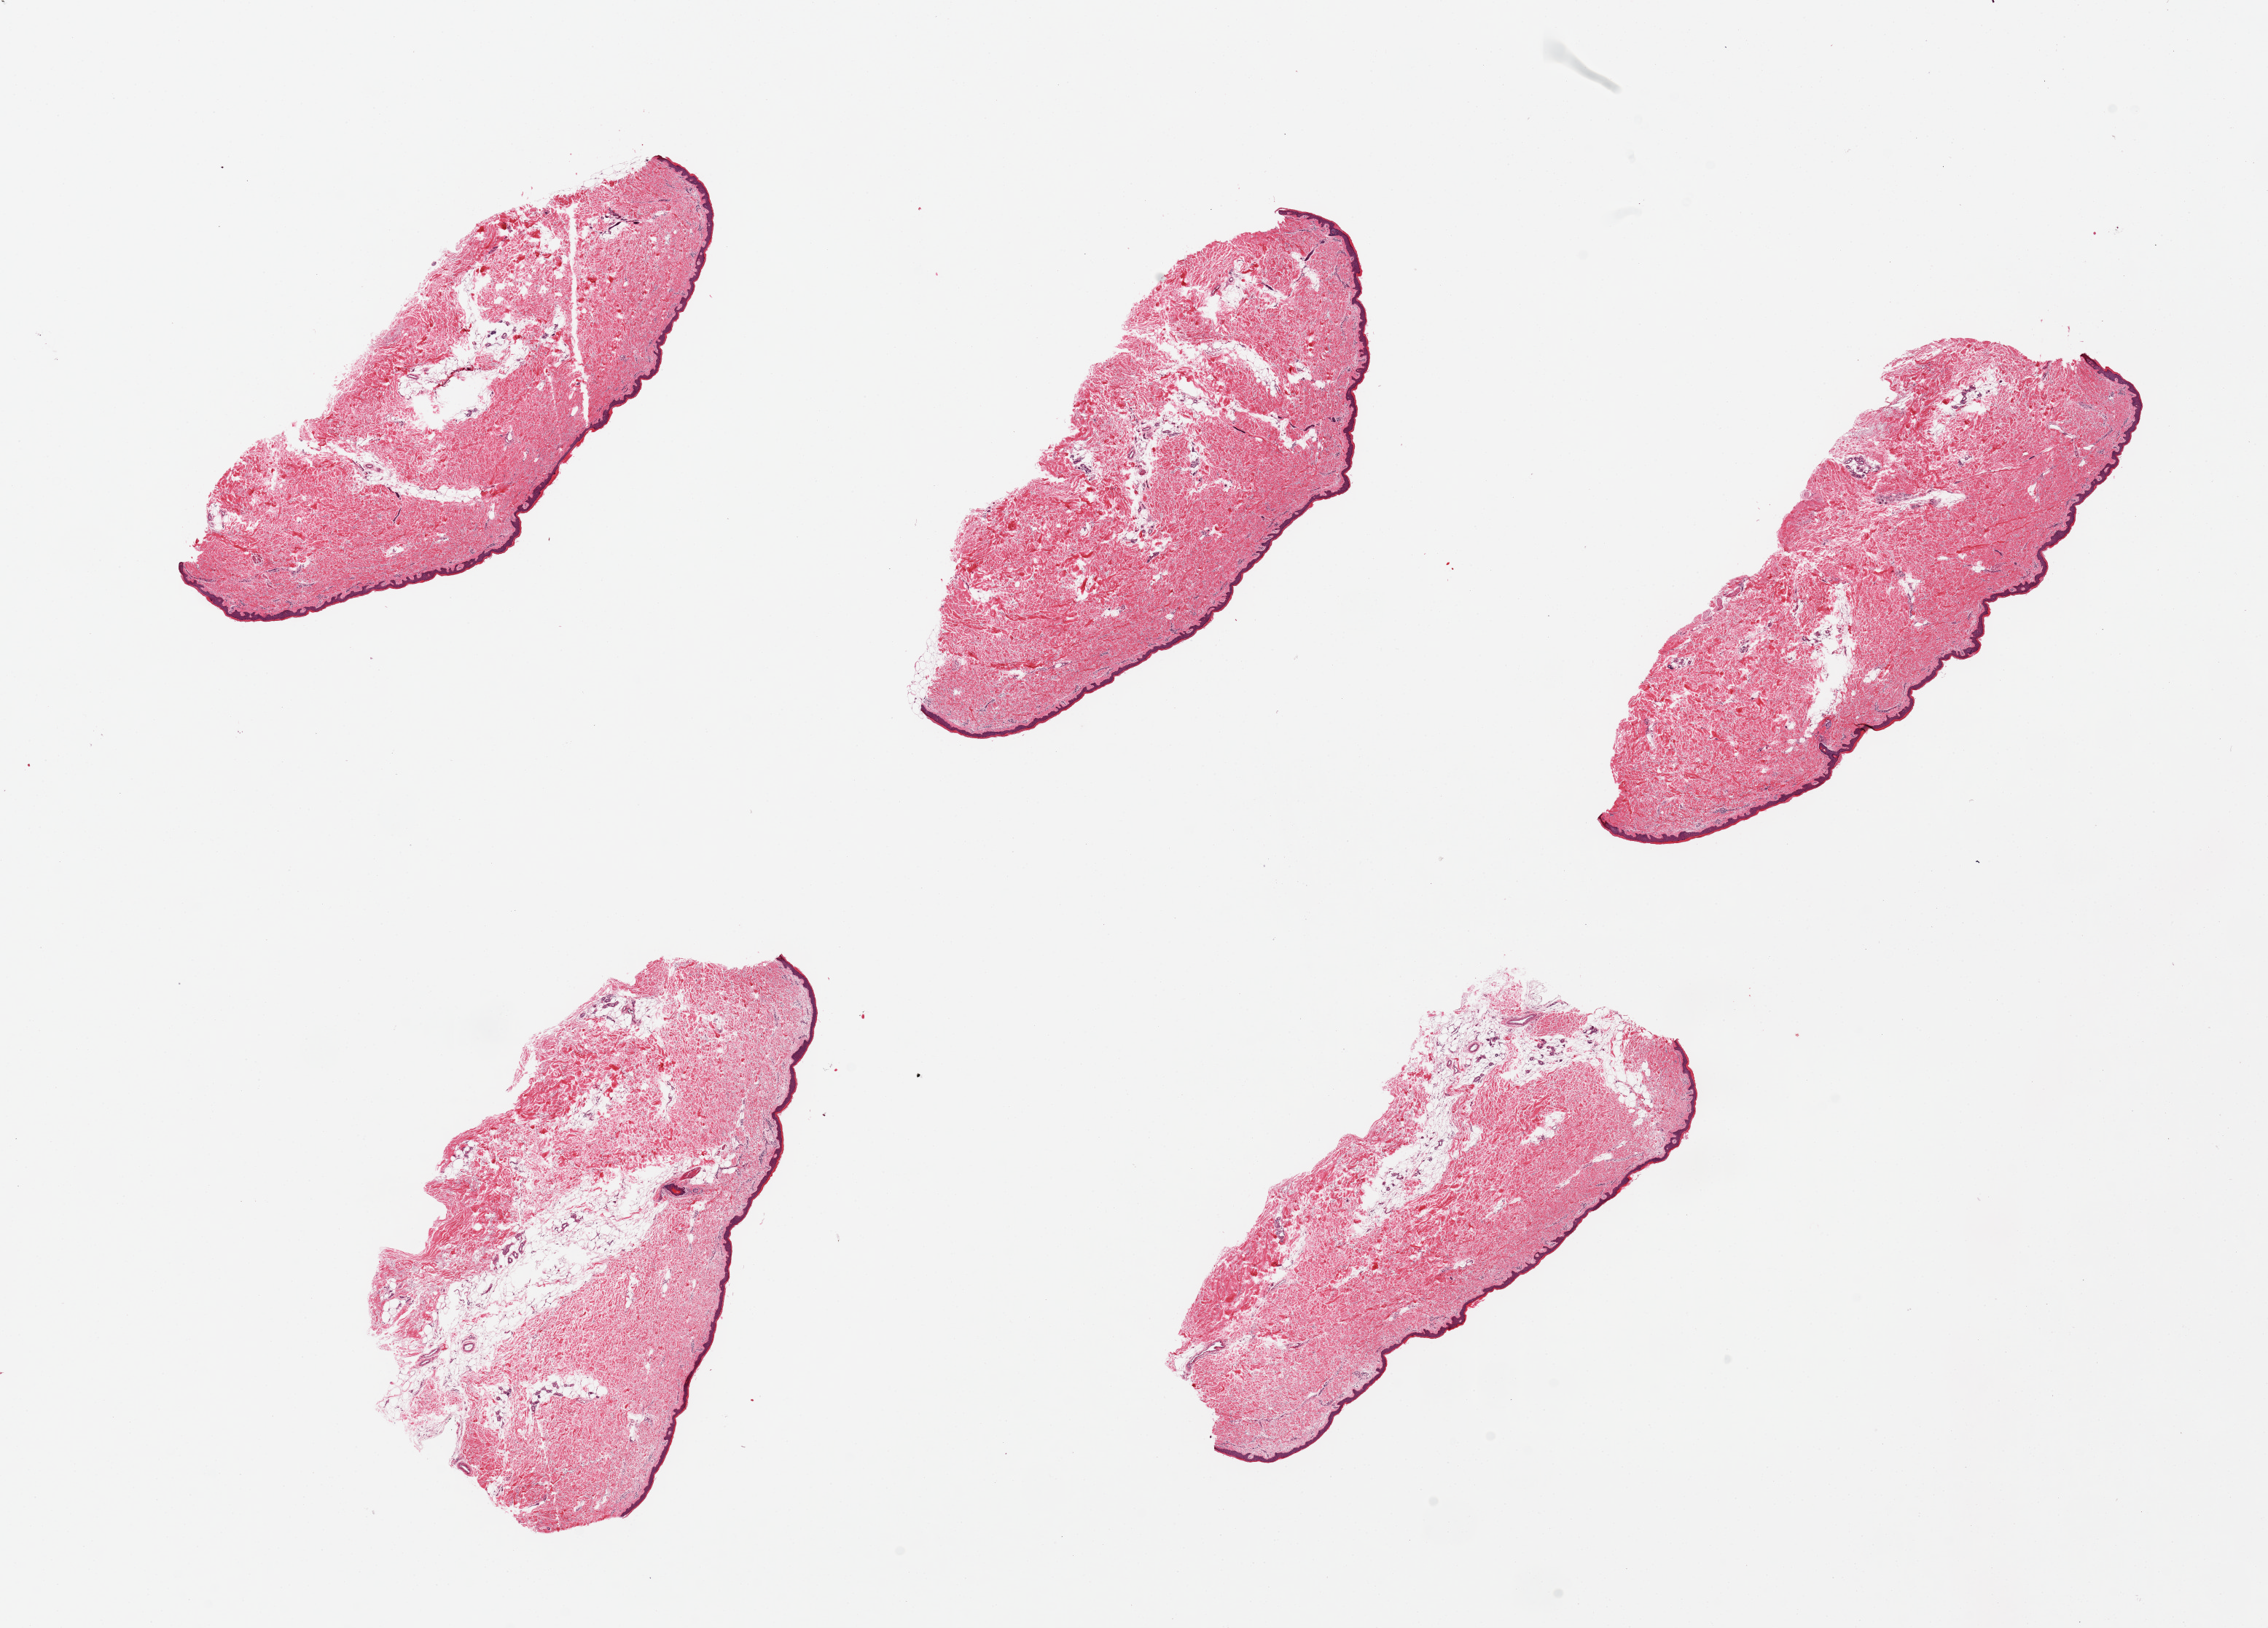
Whole-slide image, hematoxylin and eosin (H&E) stain, brightfield — a low-resolution overview of the entire scanned area, about 24.6 x 17.7 mm (acquisition: 20x scan). PAXgene-fixed, paraffin-embedded tissue. Section of skin of lower leg (target tissue). Donor tissue sample. Donor sex: female.
- review note (as recorded): 5 pieces. Squamous epithelium is ~50-60 microns thick